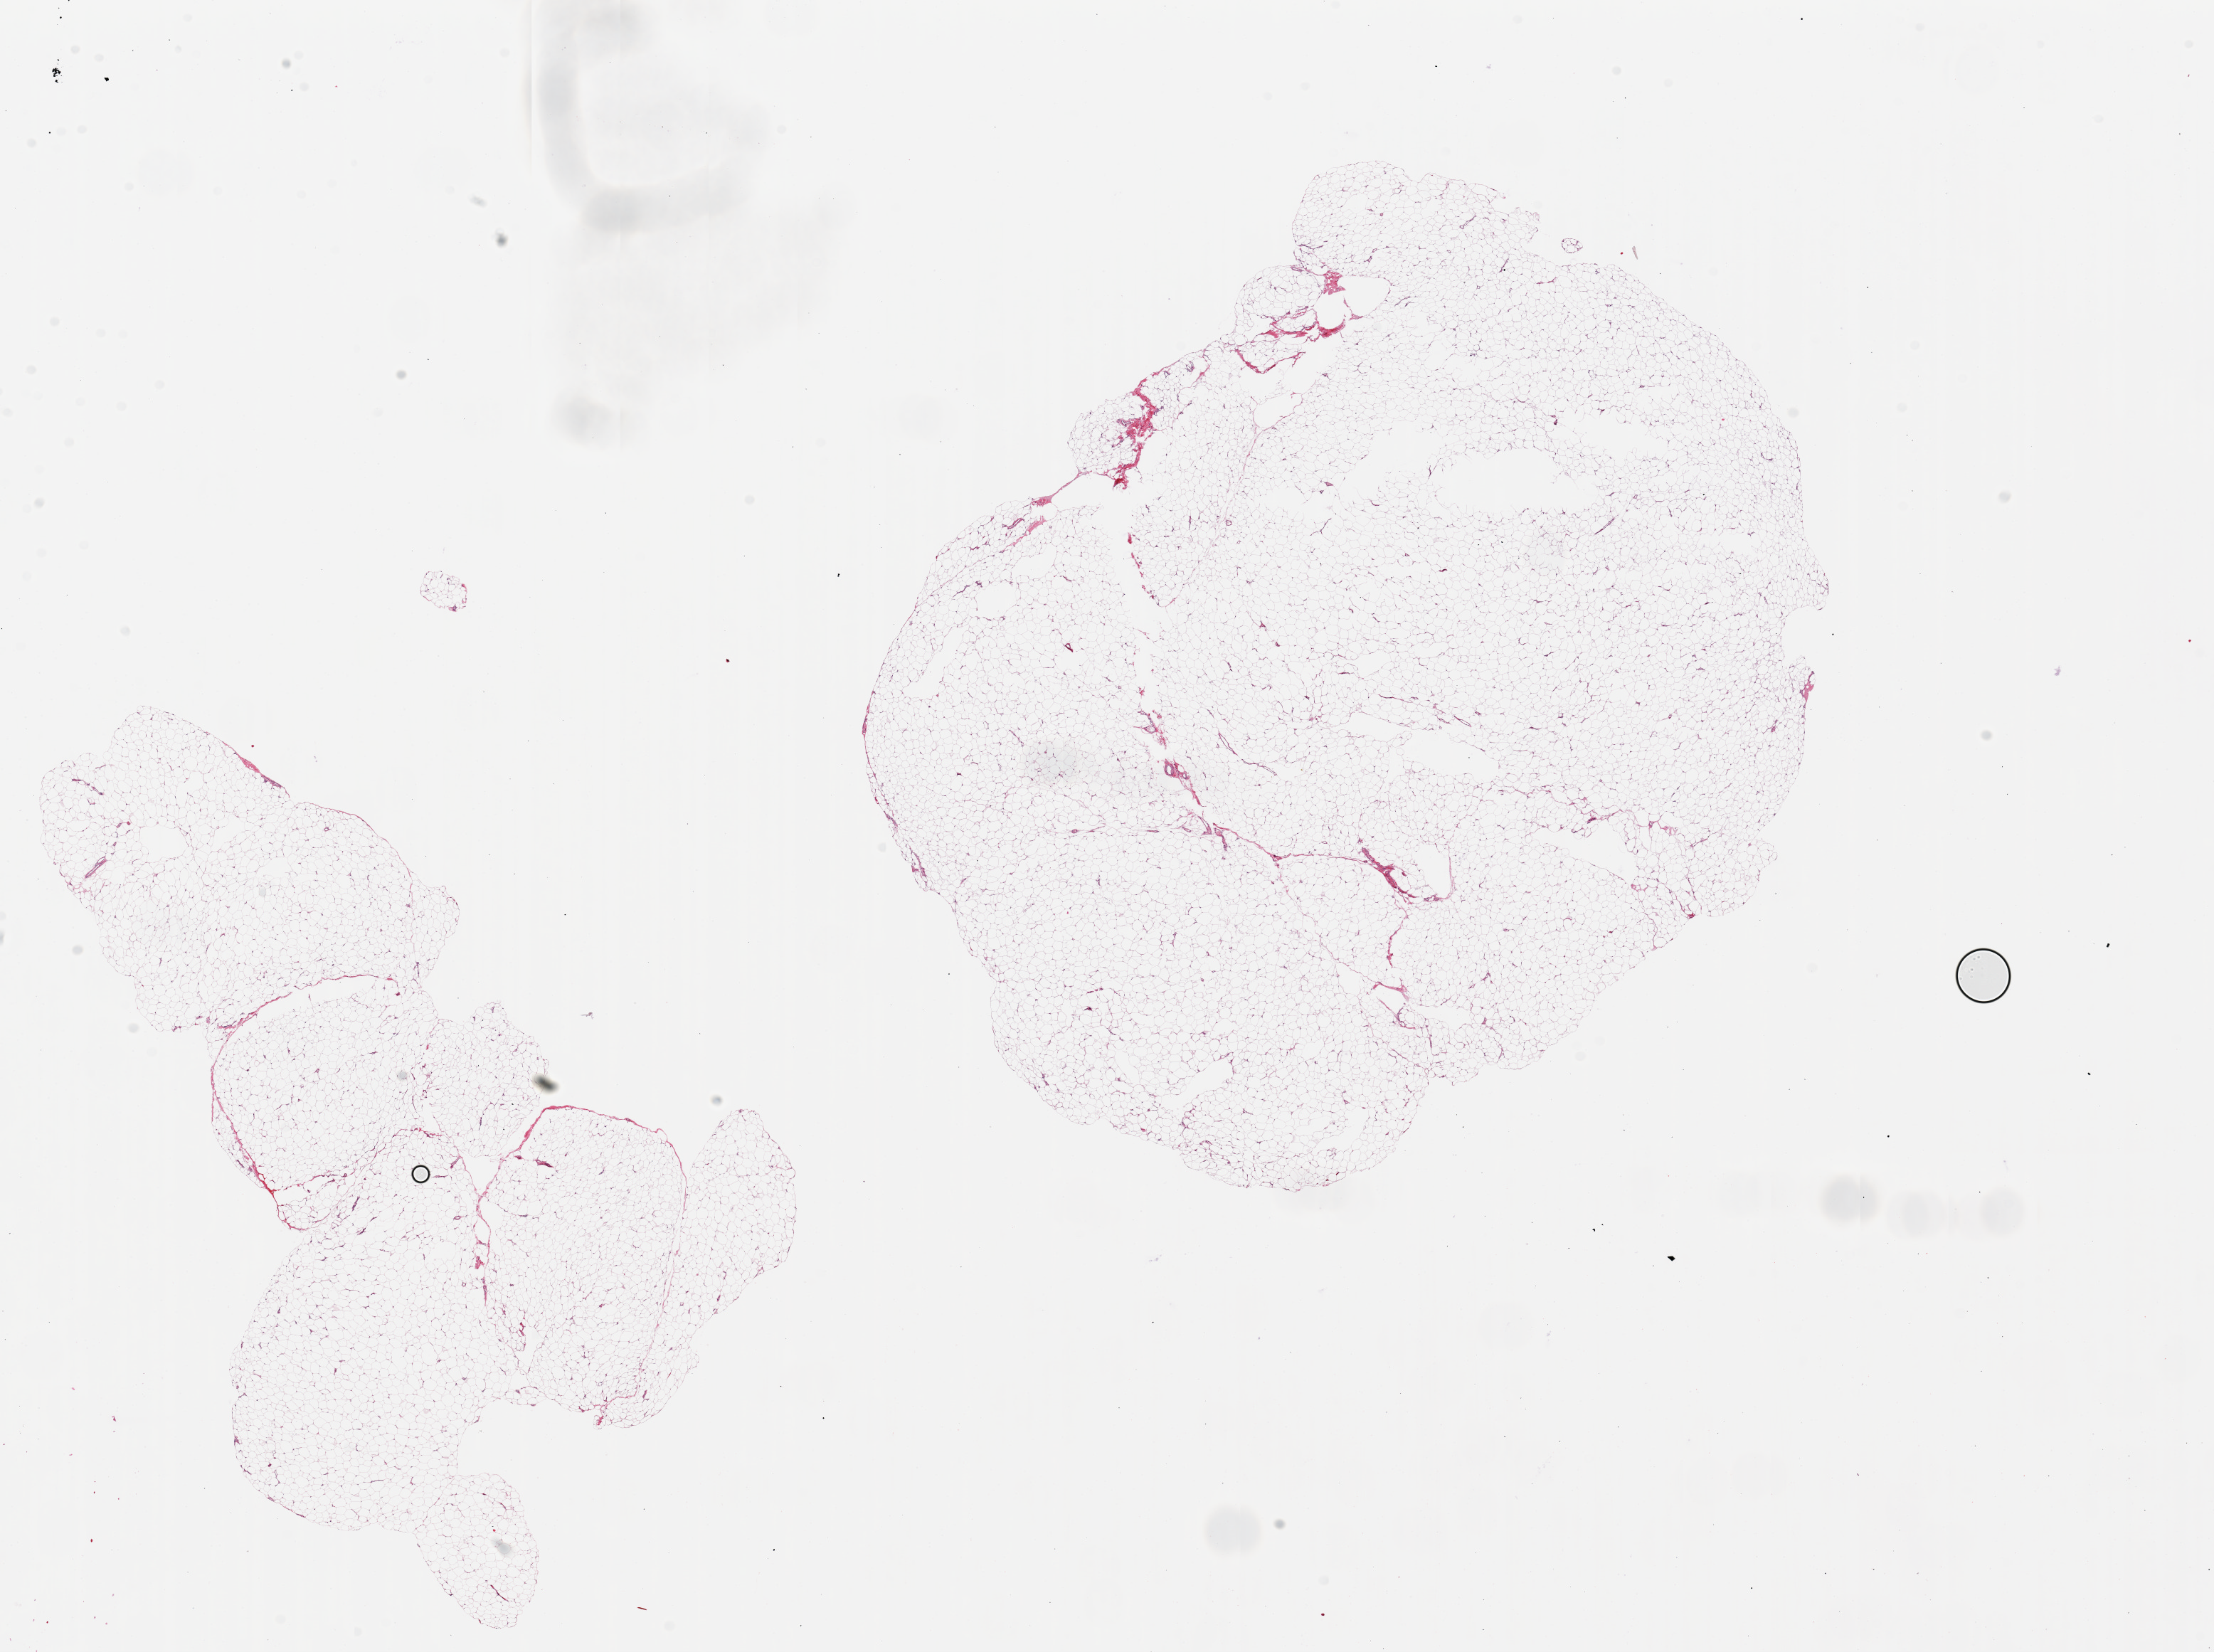
Haematoxylin and eosin whole-slide image — whole scanned area (about 24.6 x 18.4 mm, from a 20x scan) shown as a low-resolution overview. PAXgene-fixed, paraffin-embedded tissue. Section of adipose tissue (target tissue). Donor tissue sample. Donor sex: female.
Review note (as recorded): 2 pieces ~10x8mm.